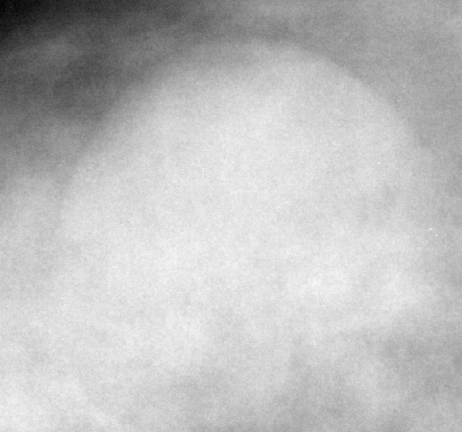
Crop from a digitized film mammogram around one marked abnormality, right breast, CC view.
Marked abnormality: mass, shape oval, margins obscured; BI-RADS assessment category 3; subtlety rating 5 on a 1 (subtle) to 5 (obvious) scale; pathology result (as recorded, not read from the image): benign.